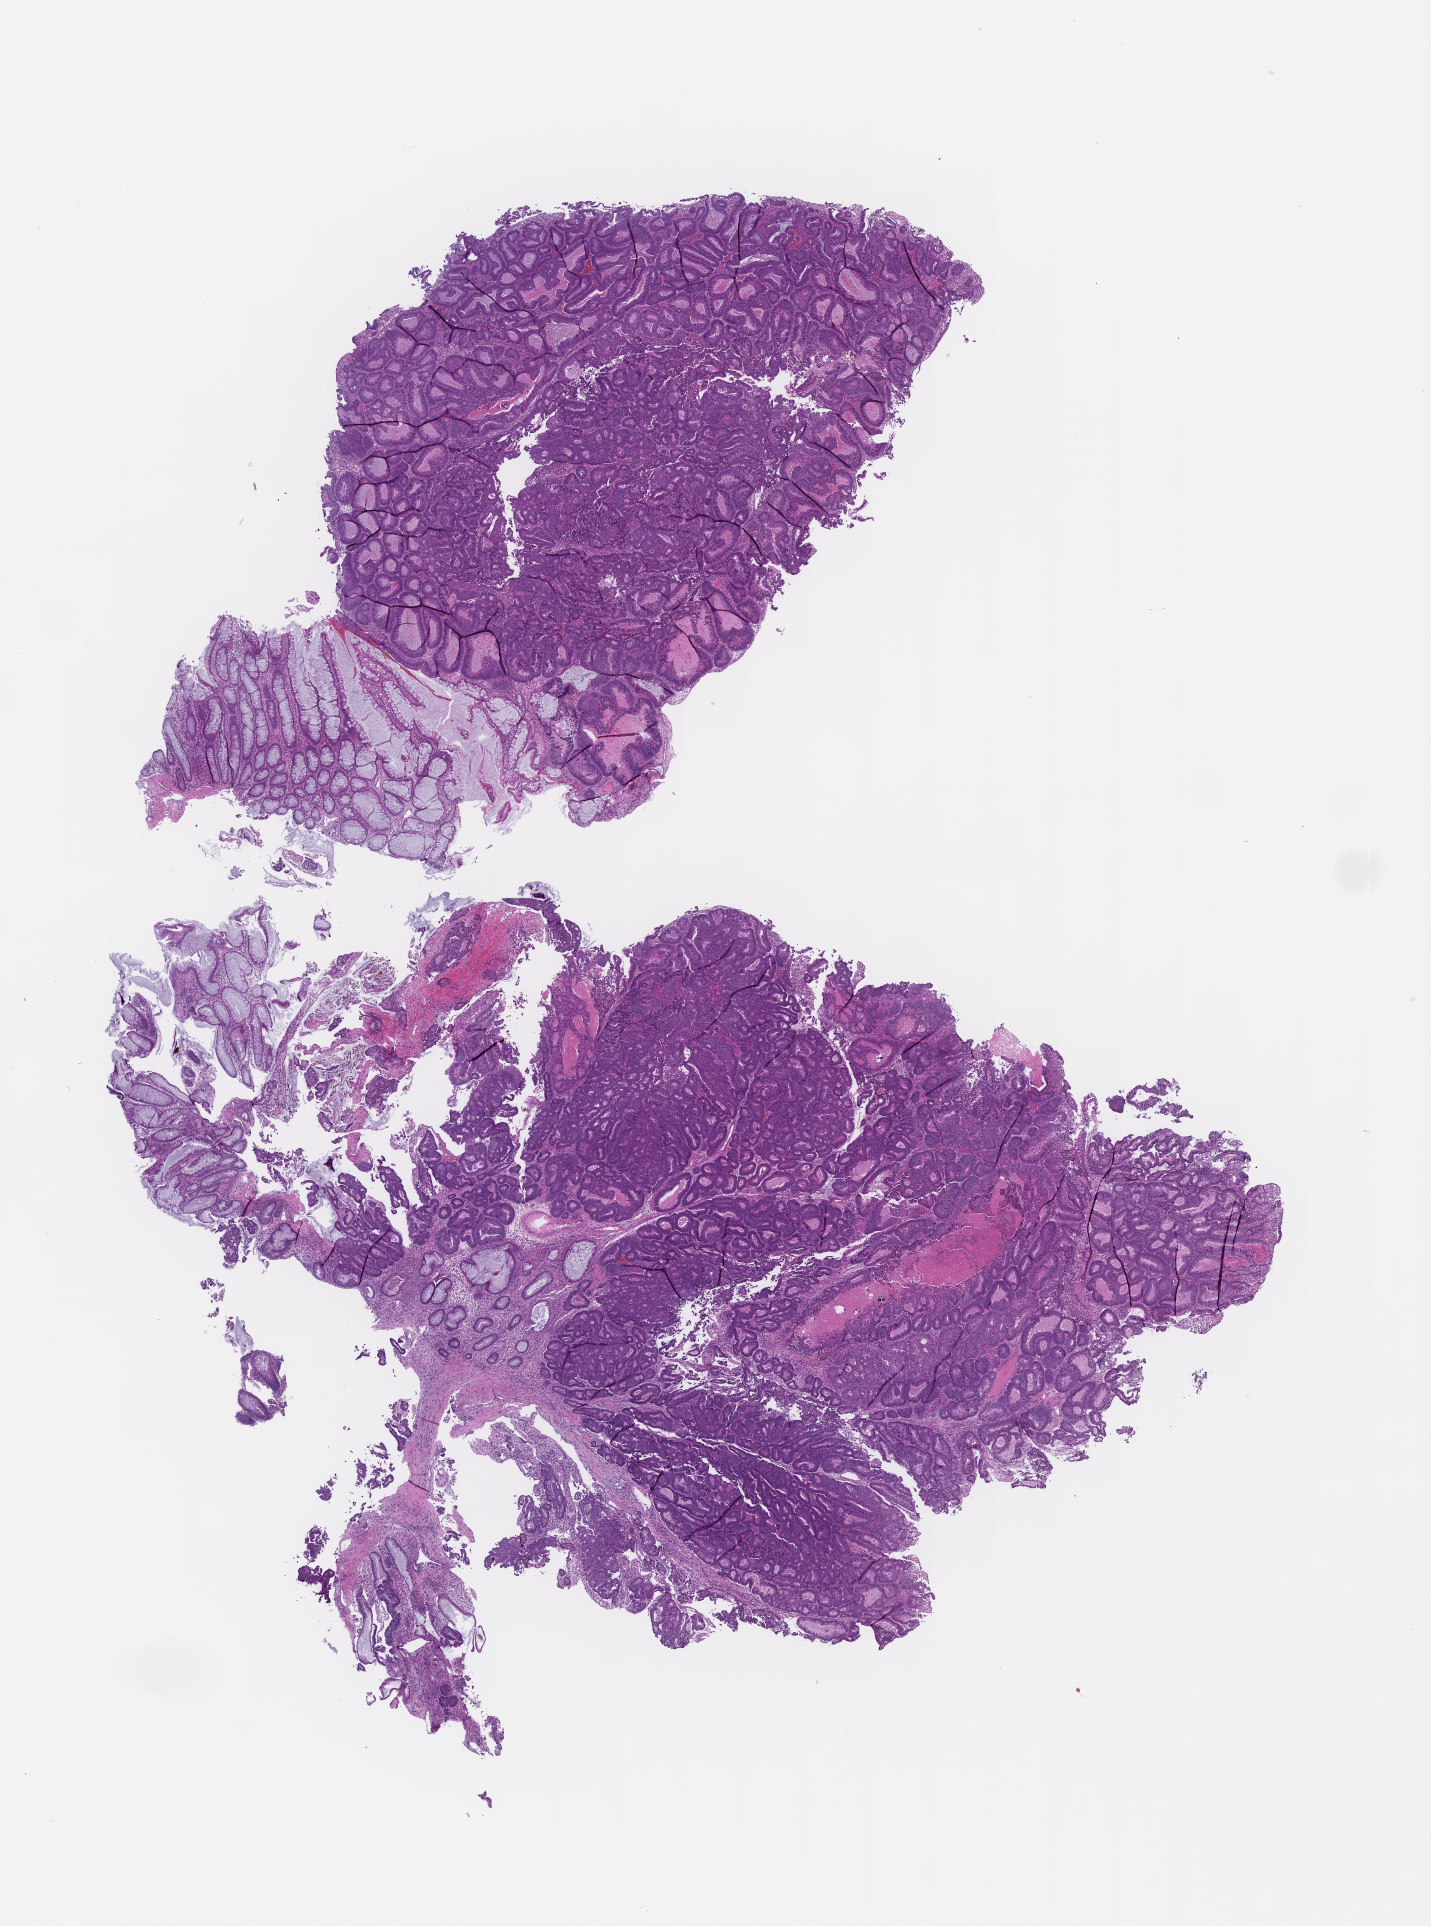
Whole-slide image, hematoxylin and eosin (H&E) stain, low-resolution overview of the scanned area, about 11.6 x 15.6 mm, formalin-fixed paraffin-embedded section, tissue site: colon, specimen time point: archival tissue. Male patient.
* this section: primary tumor
* diagnosis: Colorectal Carcinoma